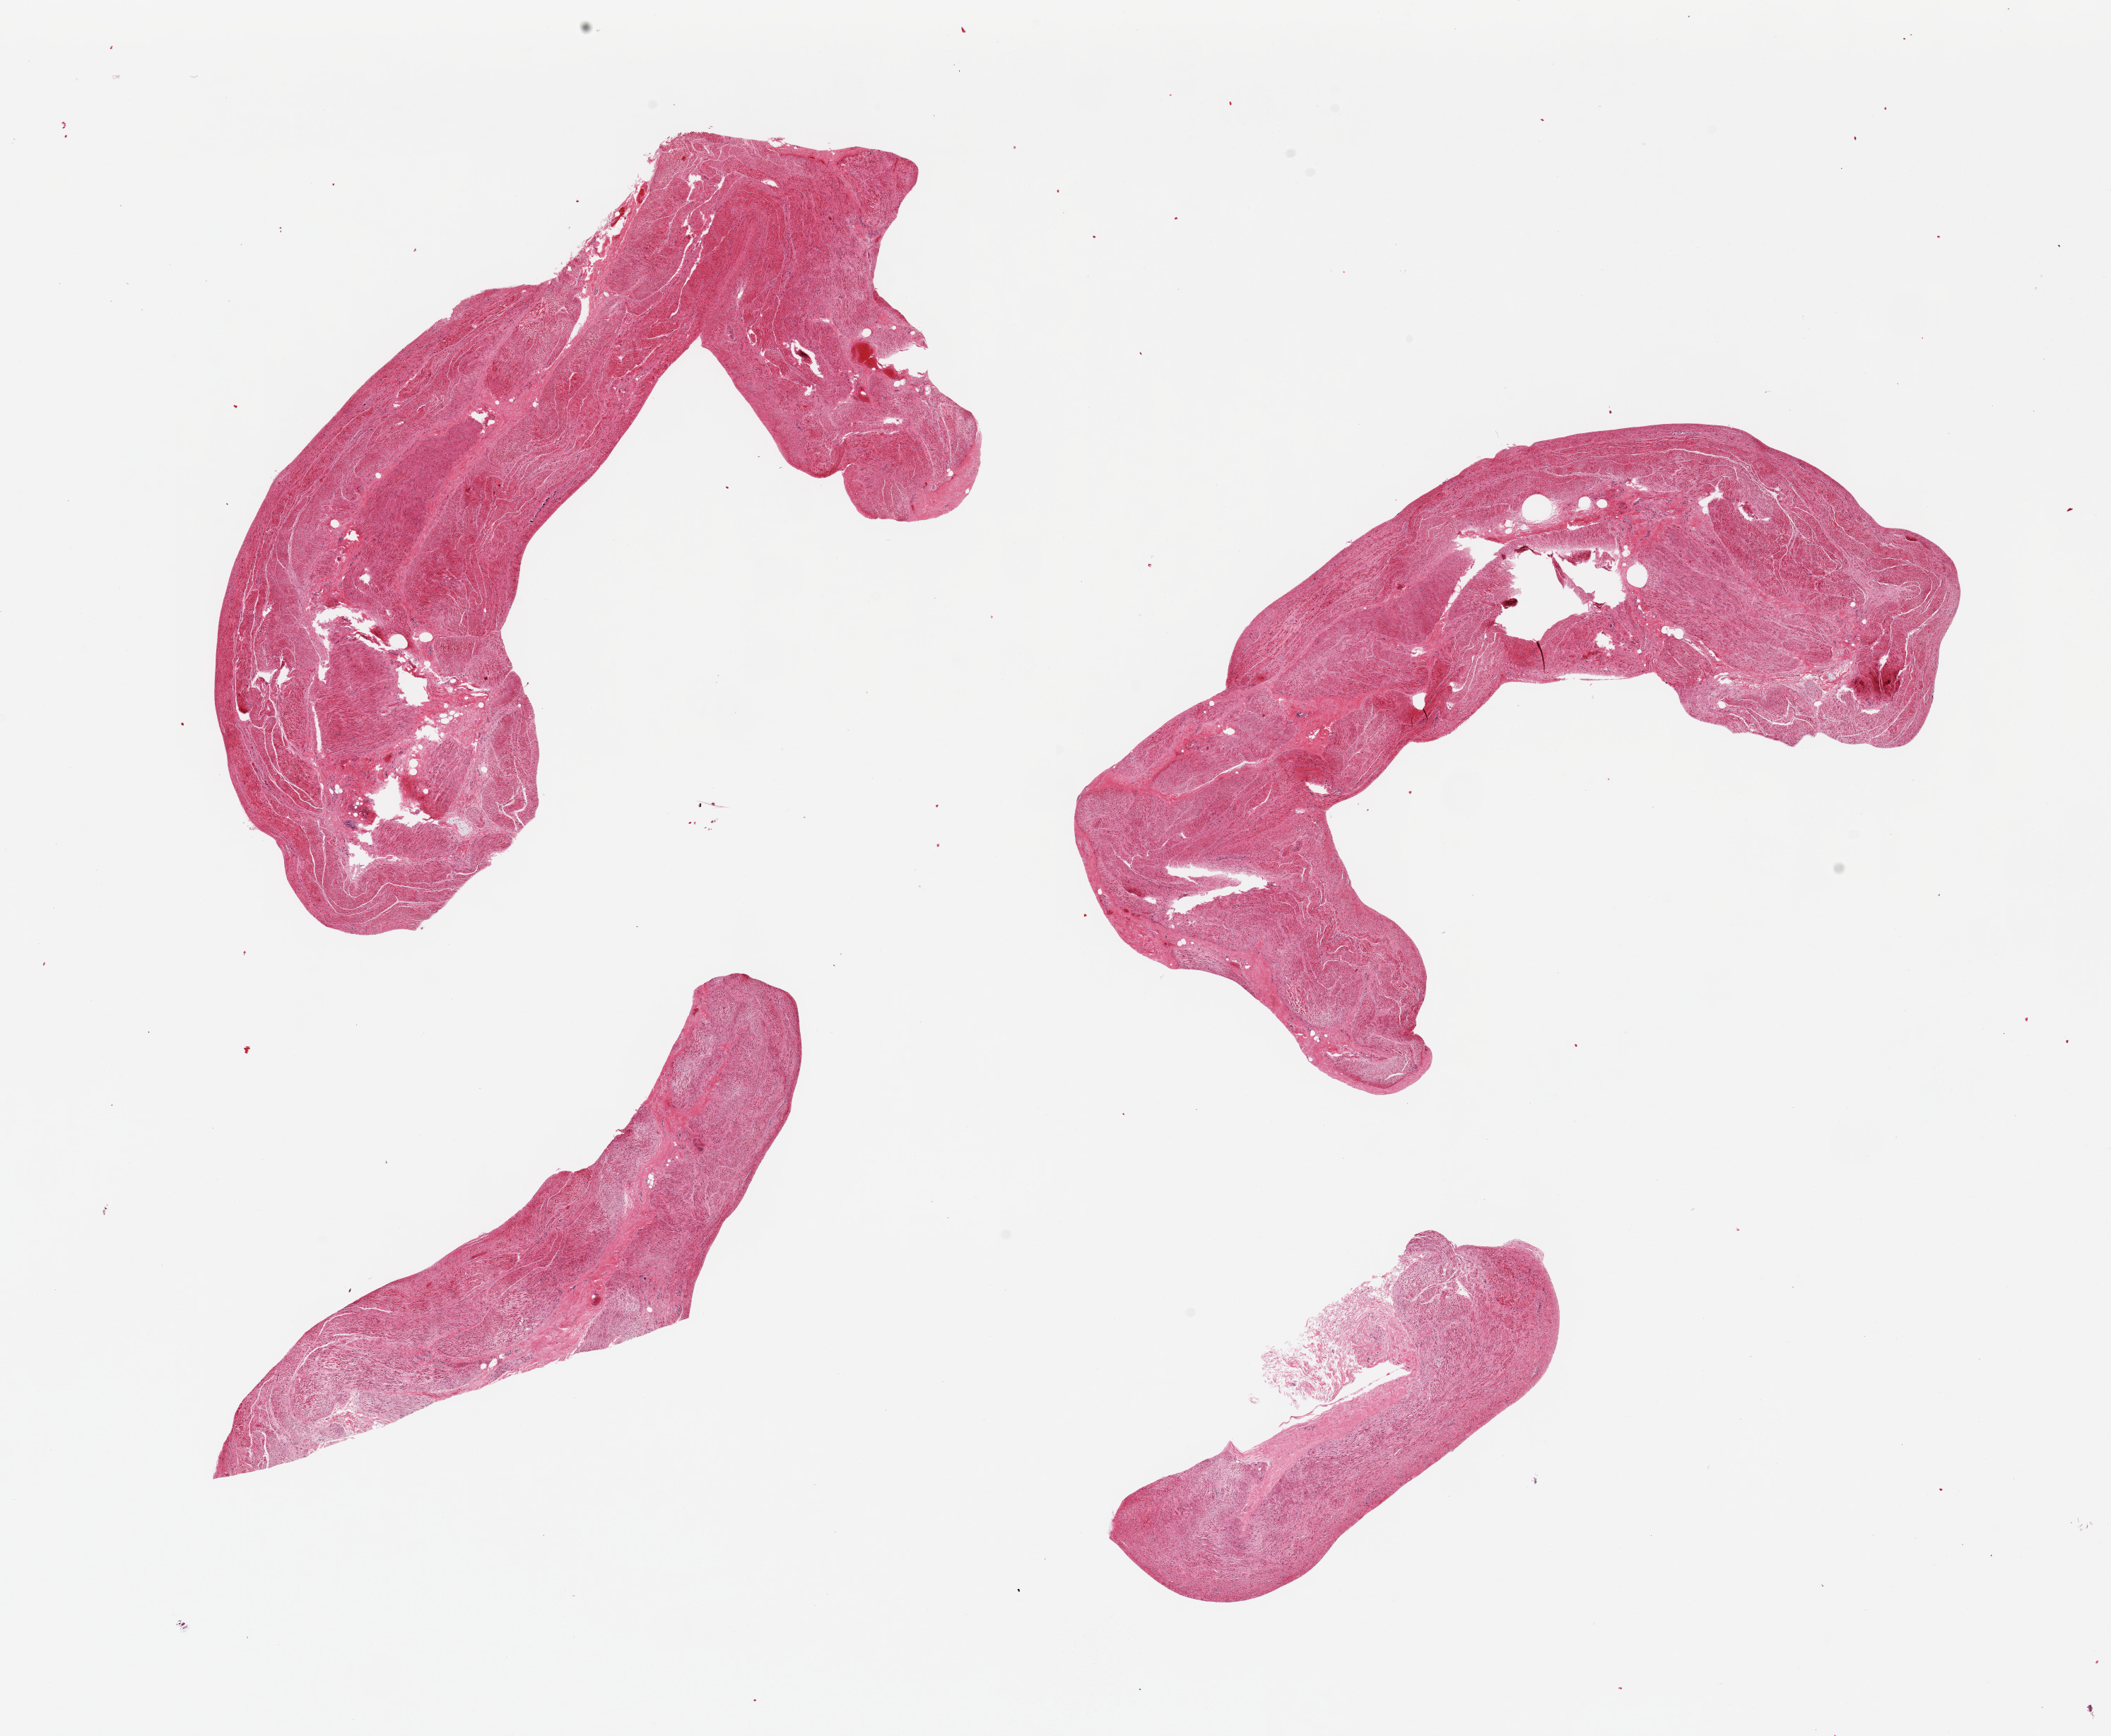
Whole-slide image, hematoxylin and eosin (H&E) stain, shown as a low-resolution overview of the whole scanned area (about 23.6 x 19.4 mm, acquisition: 20x scan); PAXgene-fixed, paraffin-embedded tissue; section of stomach (target tissue); tissue donor sample.
Reviewer comment on this tissue sample: 4 pieces; all muscle no mucosa.